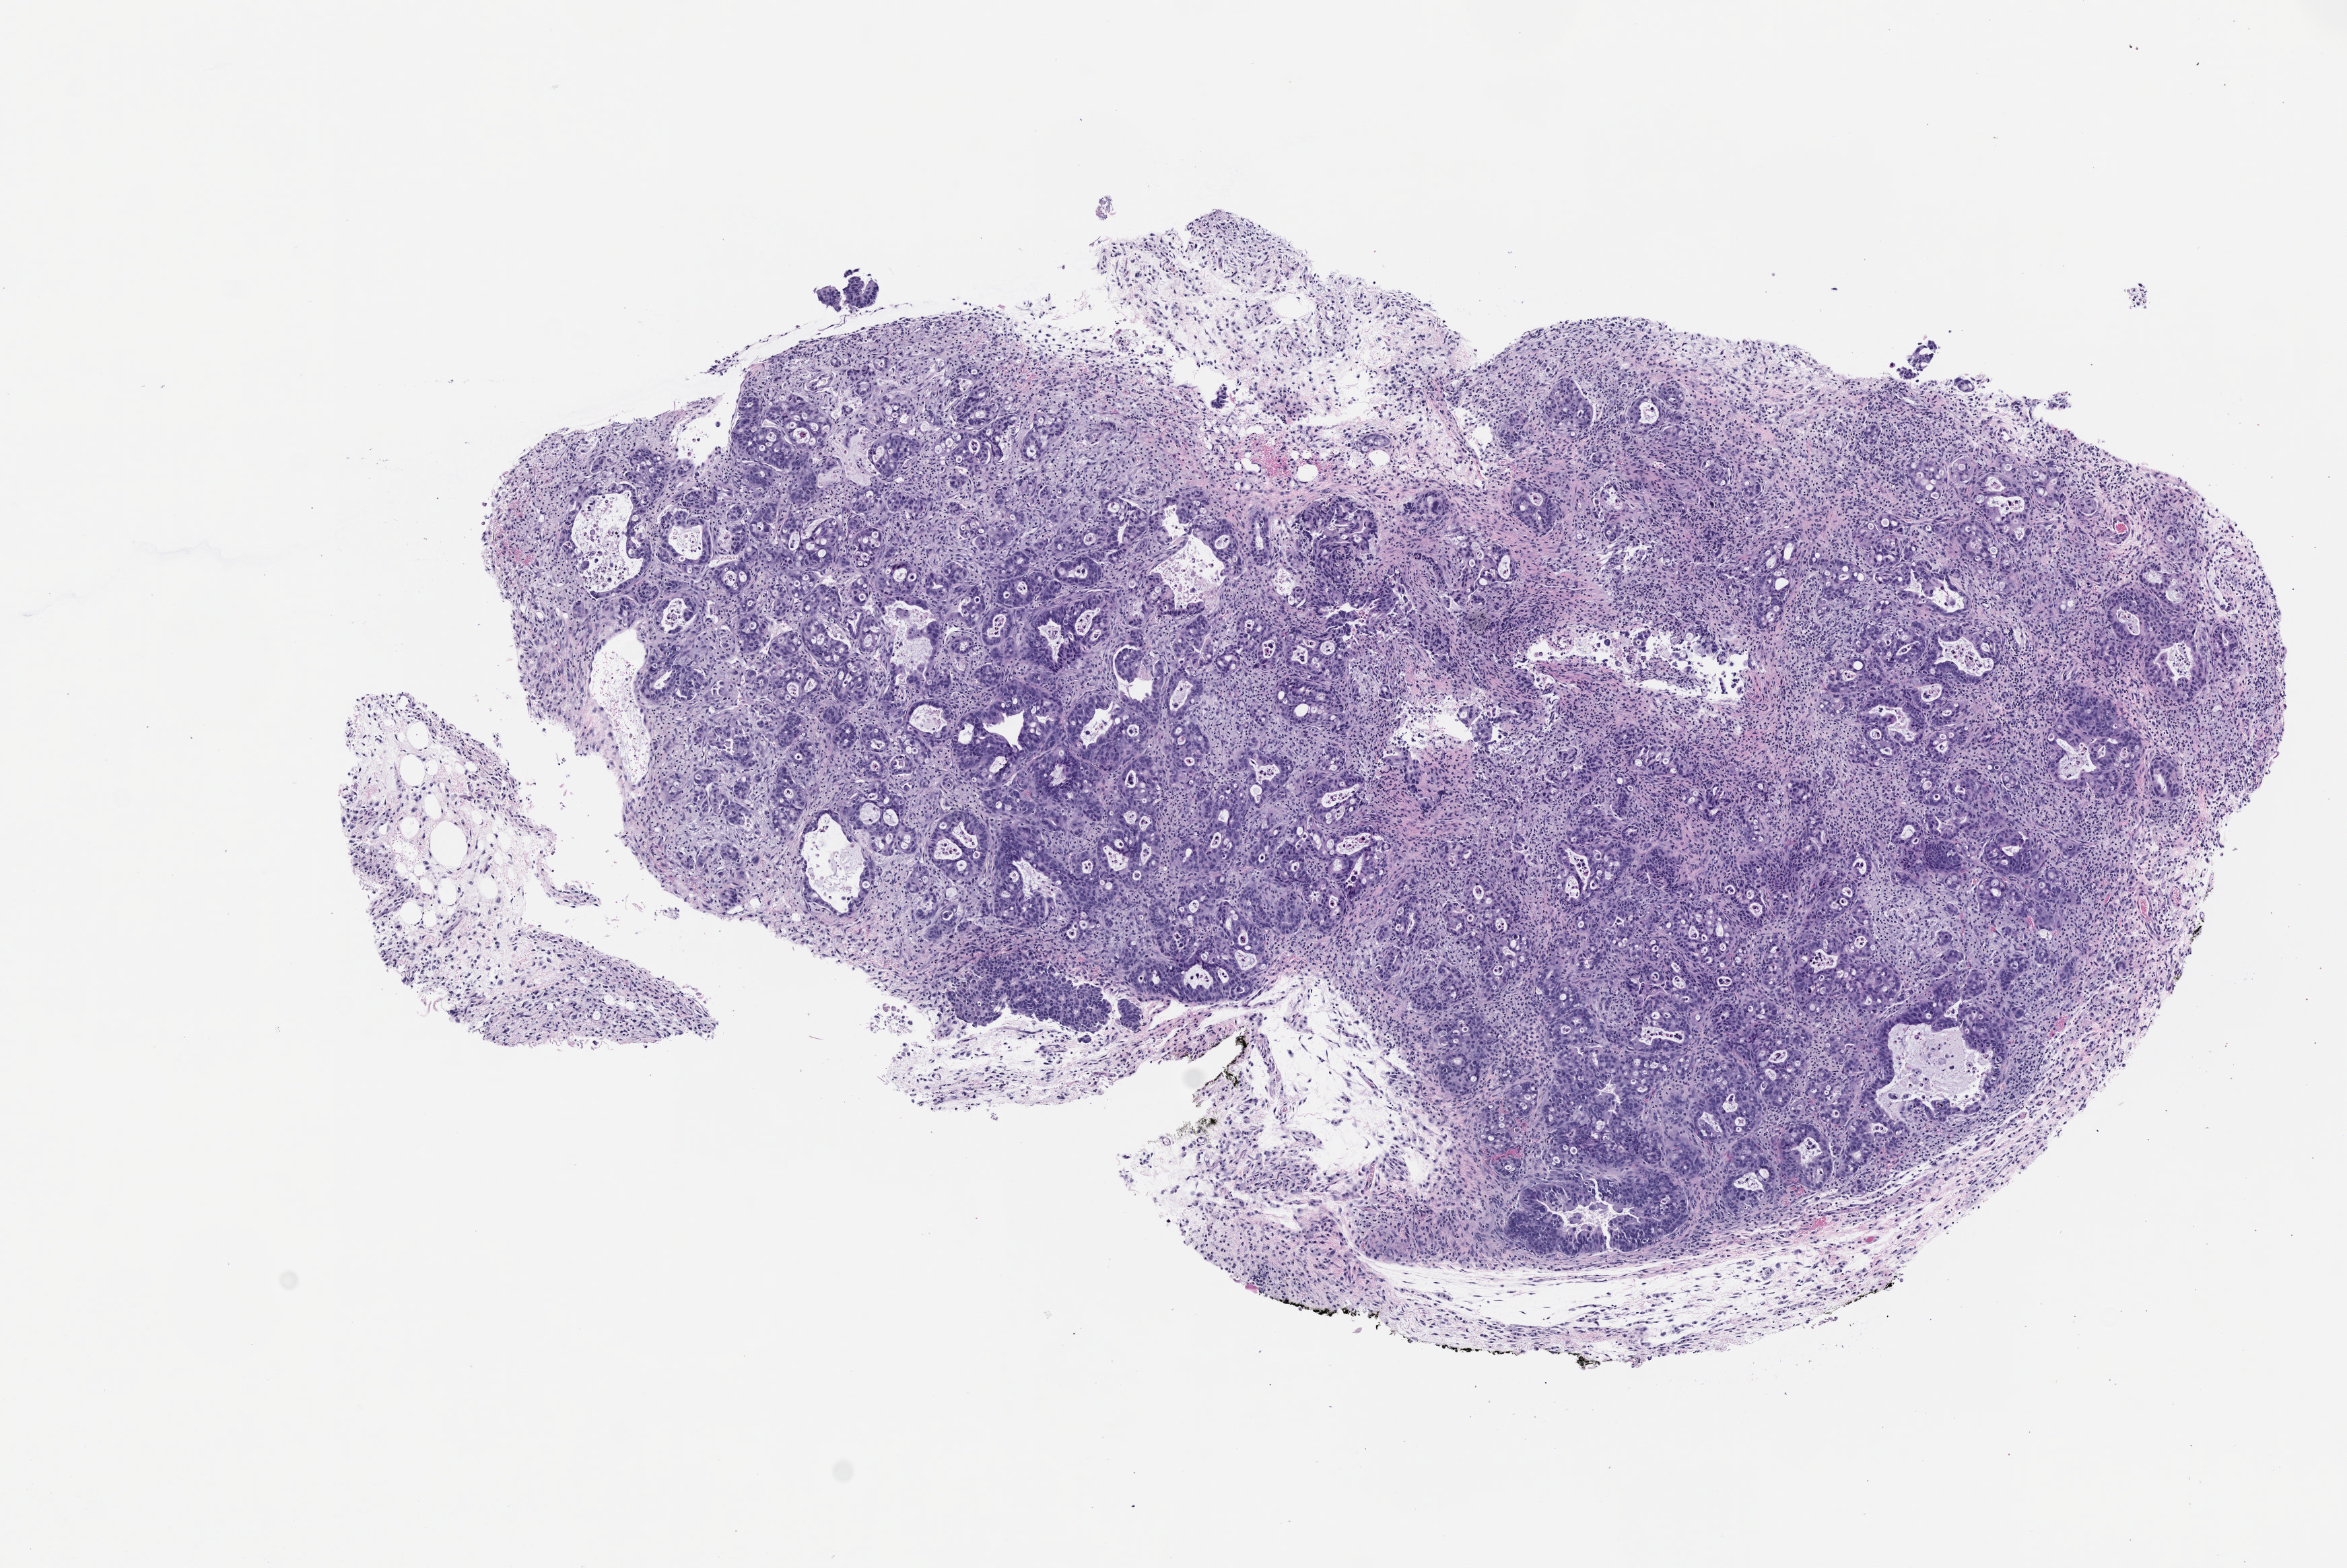
Whole-slide image, H&E: patient-derived xenograft (human tumor grown in a mouse), low-resolution overview of the scanned area, about 7.0 x 4.7 mm; formalin-fixed paraffin-embedded section; tumor site category: small intestine.
Originating patient diagnosis: Small Intestinal Adenocarcinoma.